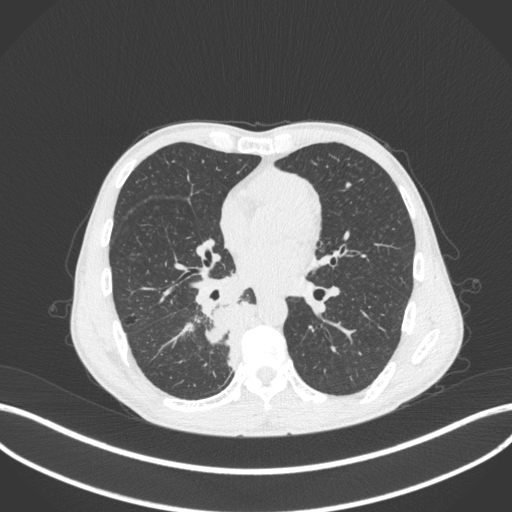
Chest CT, one axial slice; position 181 of 371 along the scan axis; lung window (W 1500 / L -600 HU); 1 mm slice thickness; 512 × 512 image matrix, field of view 400 × 400 mm. Patient: male, 58 years. Case-level facts recorded for this patient, not image findings: clinical TNM (as recorded): T3 N1 M1.
Annotated regions visible in this slice (bounding box drawn by a radiologist):
- lung tumour (recorded histology: squamous cell carcinoma): bounding box <201,301,261,375> (left, top, right, bottom; pixels)